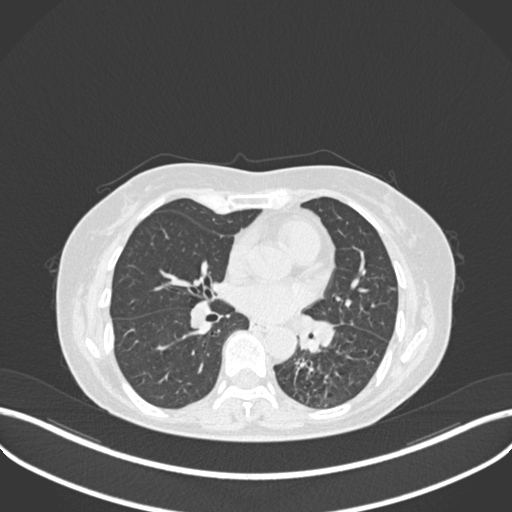
Chest CT, one axial slice; position 125 of 270 along the scan axis; reconstruction kernel B30f; lung window (W 1500 / L -600 HU); 512 × 512 image matrix, field of view 400 × 400 mm. Patient: female, 63 years. Case-level facts recorded for this patient, not image findings: clinical TNM (as recorded): T1b N0 M0; histopathological grade: G2-3.
Structures marked on this image (rectangle marked by the reading radiologist):
- lung tumour (recorded histology: adenocarcinoma): bounding box (x1, y1, x2, y2) in pixels: (283, 311, 335, 356)